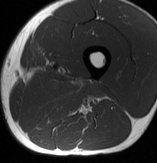
MRI of an extremity soft-tissue mass, one axial slice. Slice 26 of 70 in the series (ordered by position). MR volume resampled by the dataset authors to the PET/CT grid (not the native acquisition matrix). 3.27 mm slice thickness. 157 × 163 image matrix, field of view 153 × 159 mm. Male patient. From the clinical record (not read from this slice): histological type: extraskeletal osteosarcoma; grade: high; site of the primary tumour: left adductur.
Annotated regions visible in this slice (expert contour drawn on MRI and transferred to this co-registered scan by the dataset authors):
- gross tumour volume (mass): bounding box <26,74,107,111> (left, top, right, bottom; pixels)